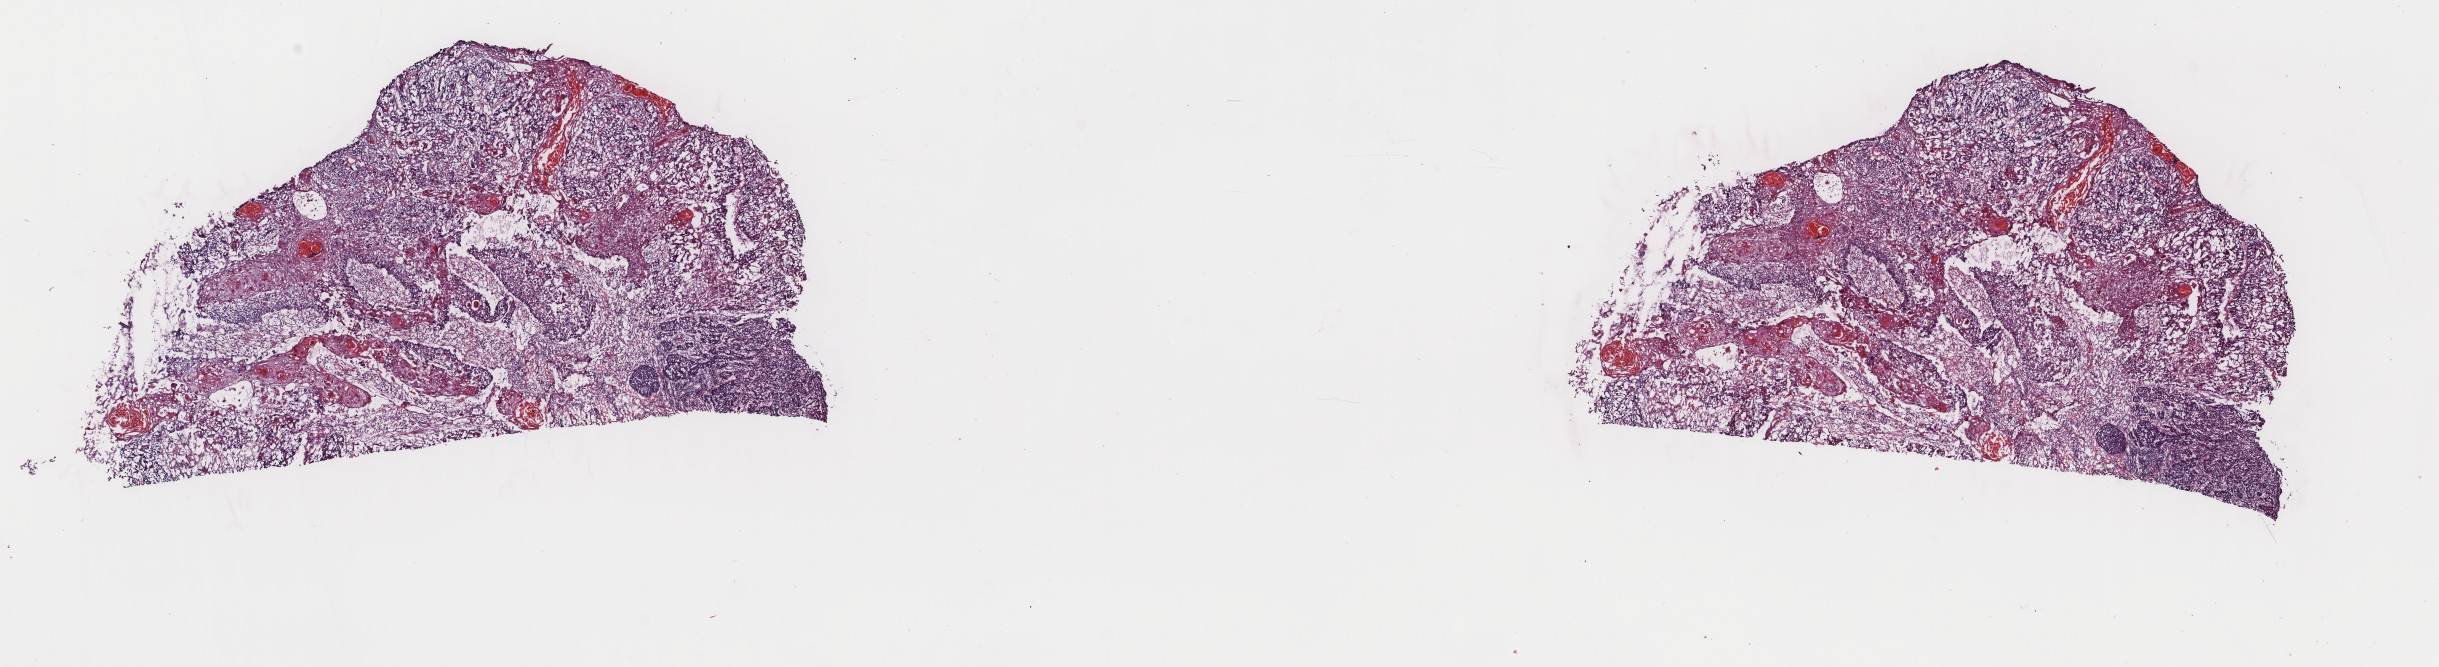
Whole-slide histology image, Hematoxylin and eosin (H&E) stained, a low-resolution overview of the entire scanned area, about 19.4 x 5.3 mm (acquisition: 40x scan); frozen section from the top of the tissue portion; esophagus, primary tumour sample. Patient: male, age at initial diagnosis 61 years. Histologic grade: G2 (moderately differentiated). Composition of this section per pathologist review: tumour cells 70%, tumour nuclei 70%, normal cells 0%, stromal cells 29%, necrosis 1%. Inflammatory infiltration, as recorded: lymphocyte infiltration 6%, monocyte infiltration 3%, neutrophil infiltration 4%.
* lymph nodes positive (case pathology): 2 of 2 examined
* pathologic diagnosis: Squamous cell carcinoma, NOS
* AJCC pathologic stage: III (6th edition)